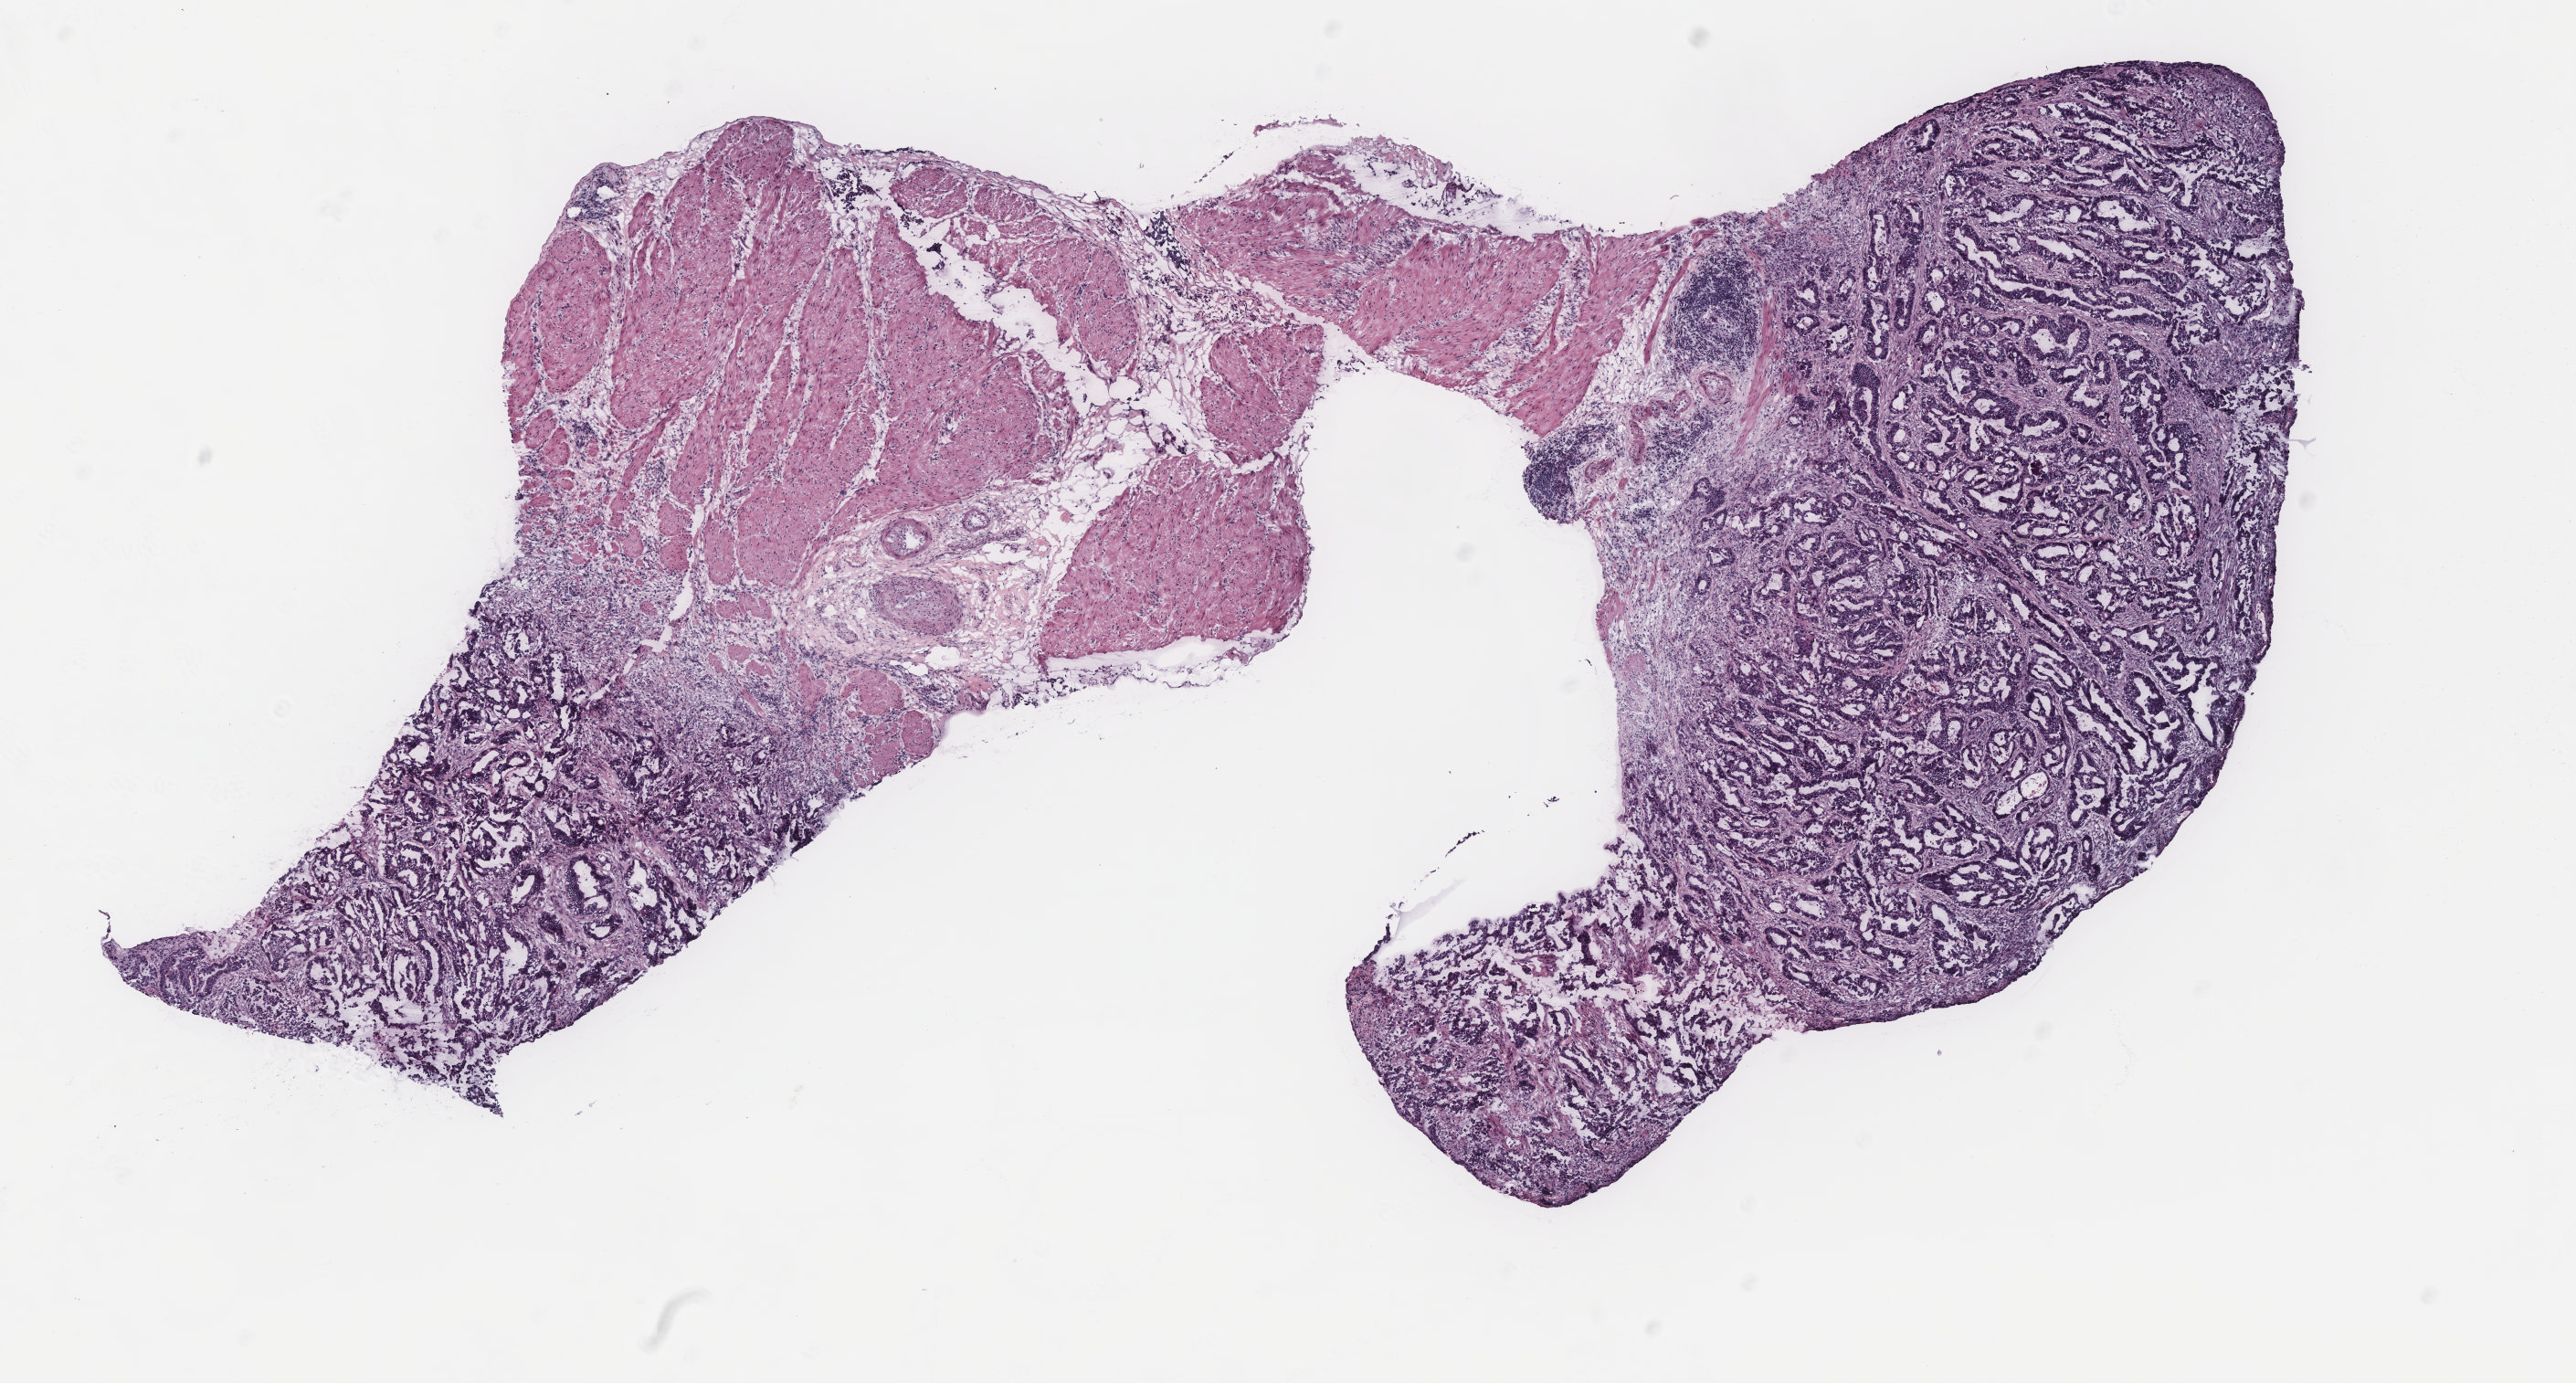
H&E-stained whole-slide image — a low-resolution overview of the entire scanned area, about 11.3 x 6.1 mm, colon, tissue type not recorded.
- patient diagnosis (cohort enrolment): colon cancer (colon)